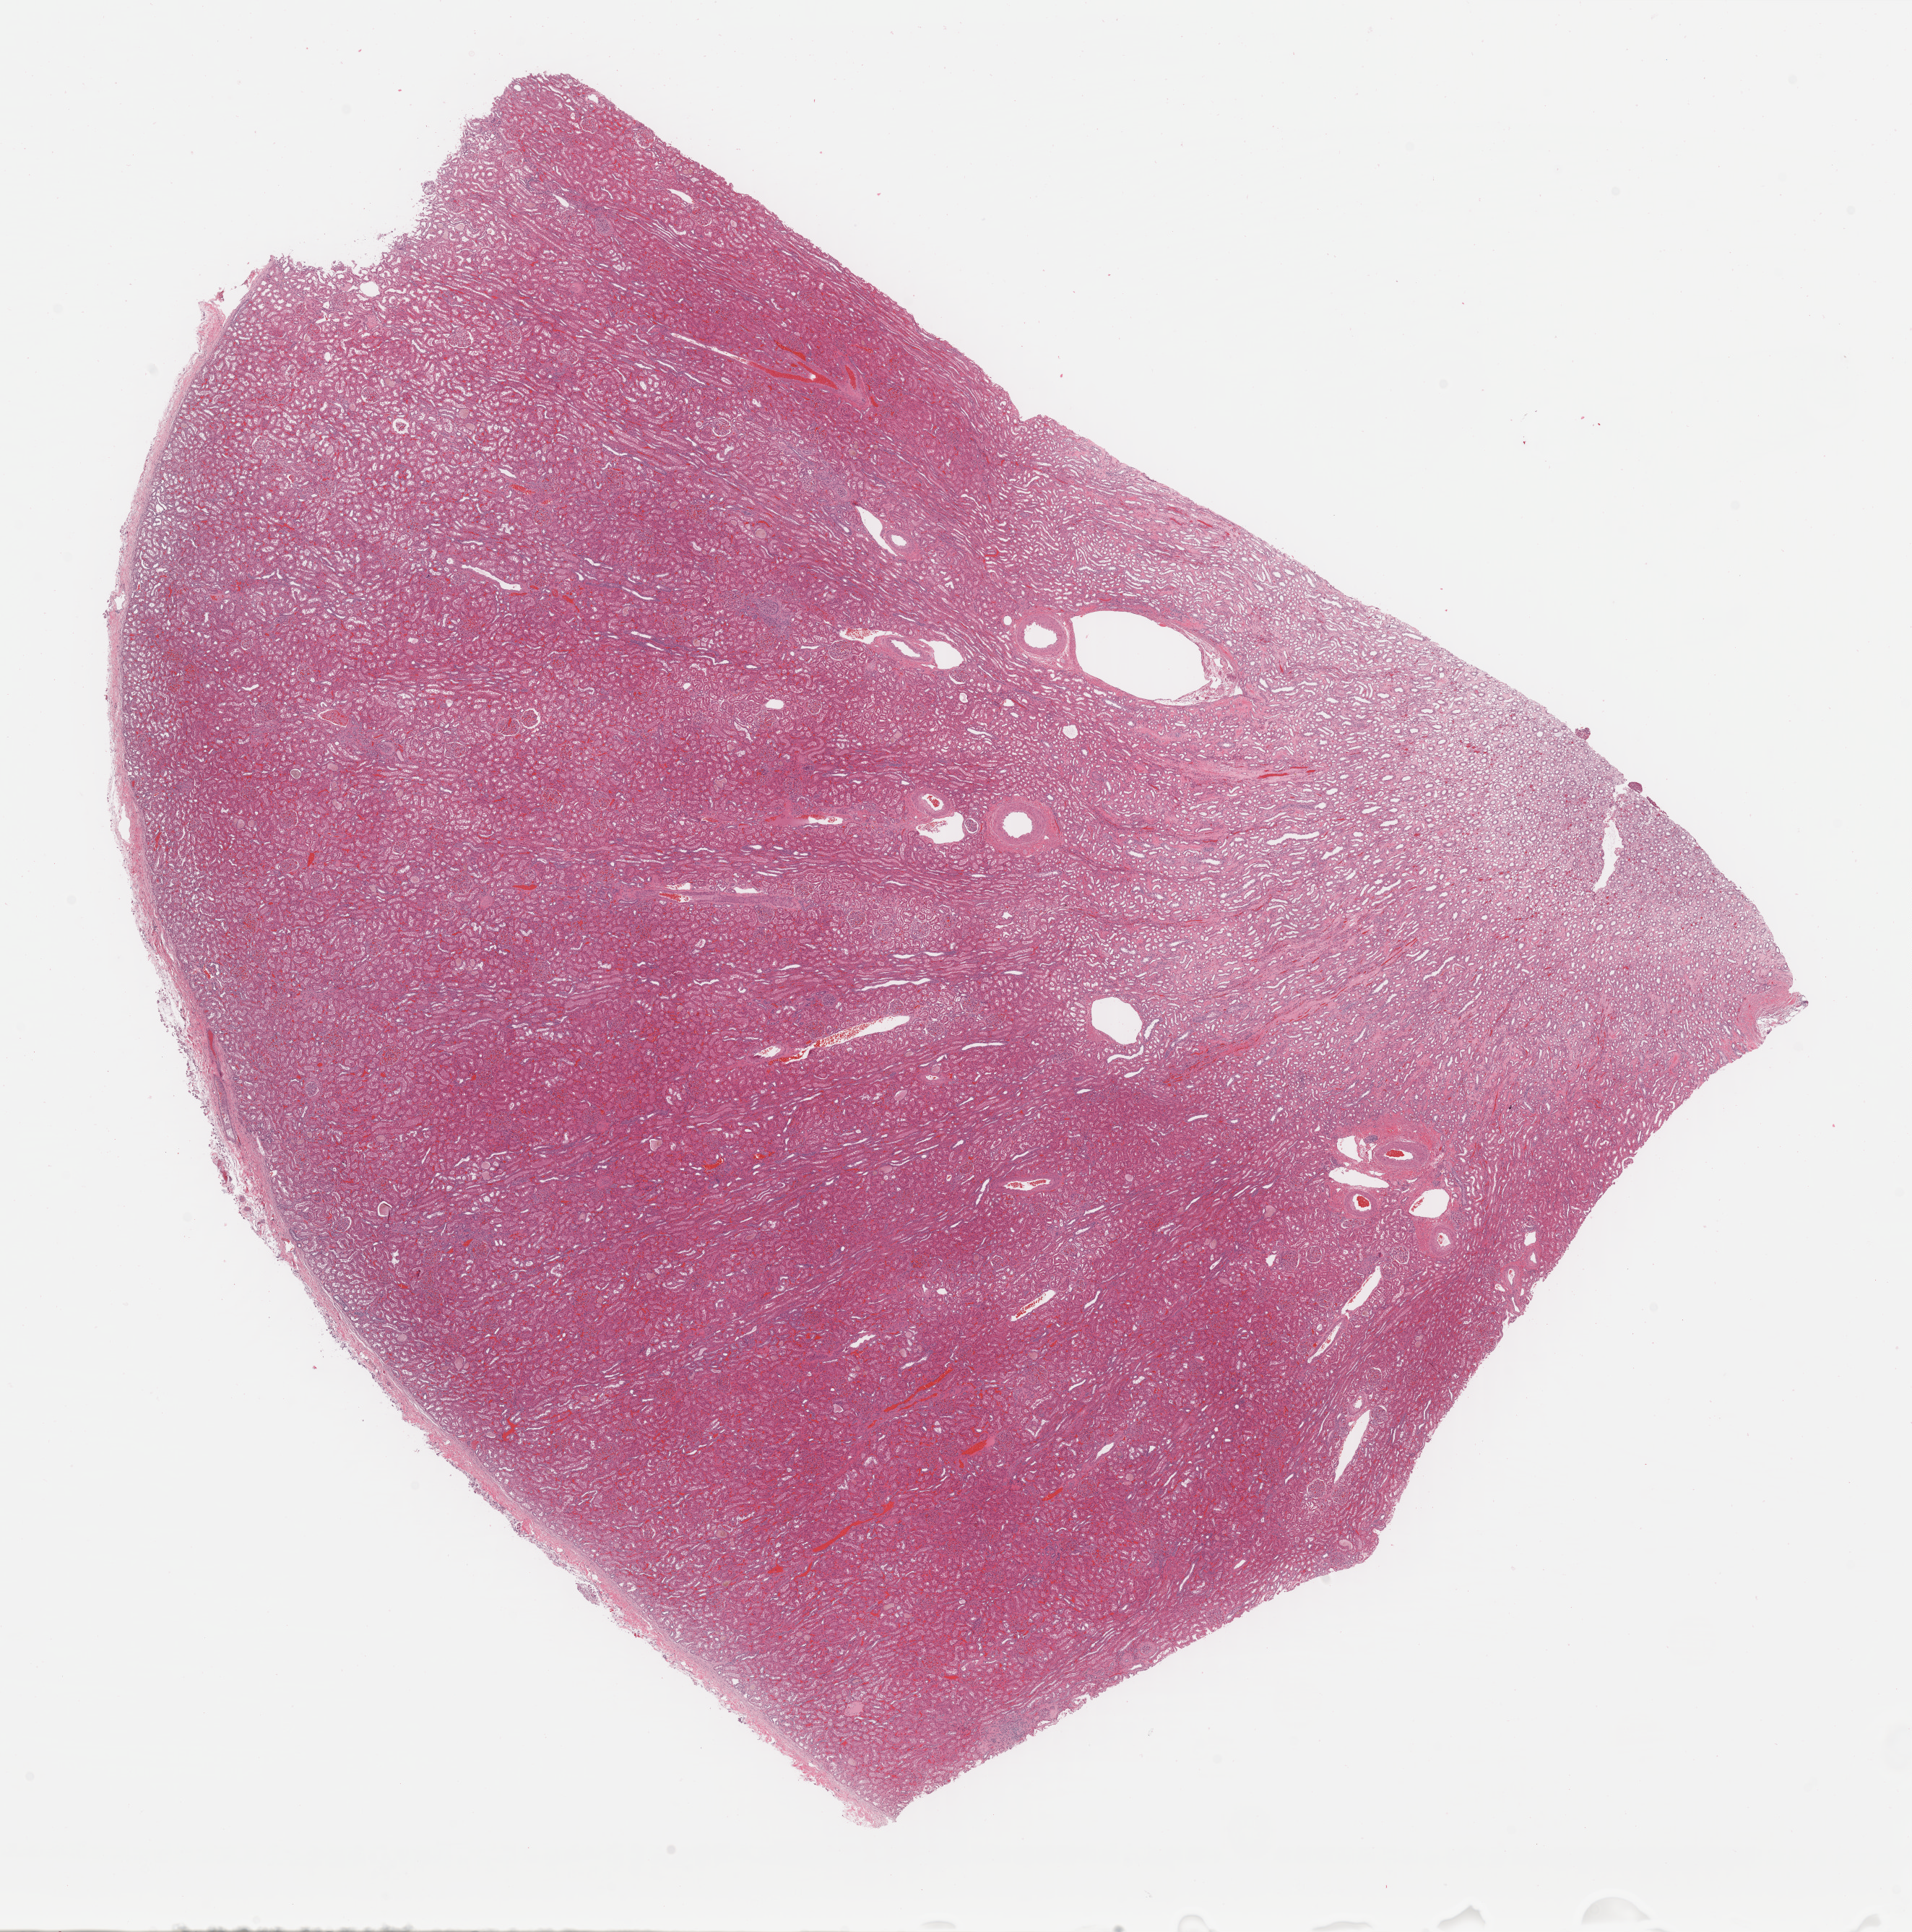
Digitized Hematoxylin and eosin (H&E) stained tissue section (whole slide) — whole scanned area (about 20.9 x 21.2 mm, slide scanned at 40x) shown as a low-resolution overview. Formalin-fixed paraffin-embedded (FFPE) diagnostic section. Sample: solid tissue normal (non-tumour tissue), kidney. Male, age 45 years at initial diagnosis. Composition of this section per pathologist review: tumour cells 0%, tumour nuclei 0%, normal cells 100%, stromal cells 0%, necrosis 0%. Infiltration values recorded for this section: lymphocyte infiltration 0%, monocyte infiltration 0%, neutrophil infiltration 0%.
This section: solid tissue normal sample (biorepository sample class). Patient diagnosis: Renal cell carcinoma, chromophobe type.